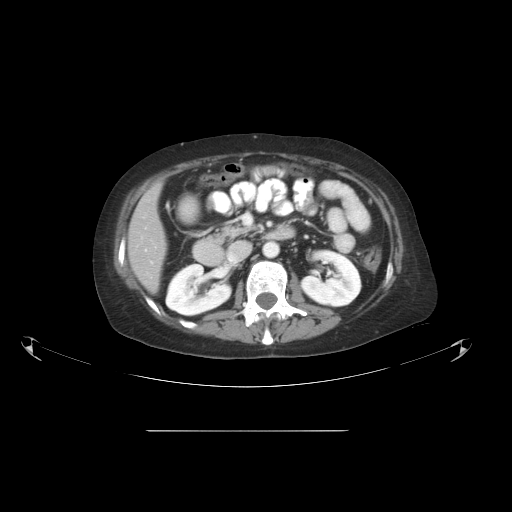
Contrast-enhanced abdominal CT, one axial slice; slice 24 of 51 in the series (ordered by position); reconstruction kernel STANDARD; 120 kVp; soft-tissue window (W 400 / L 40 HU); 5 mm slice thickness; 512 × 512 image matrix, field of view 475 × 475 mm. Female patient, age 48 years. Case-level facts recorded for this patient, not image findings: diagnosis: colorectal cancer liver metastases, imaged before liver resection; multiple liver metastases: yes; largest metastasis: 1 cm; disease in both lobes: no.
Annotated regions visible in this slice (manually delineated by an expert):
- liver: bounding box [x1, y1, x2, y2] px = [129, 187, 167, 293]
- planned liver remnant (the part of the liver to remain after resection): [129, 187, 167, 293]